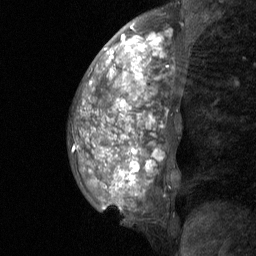
Breast MRI (dynamic contrast-enhanced), one sagittal slice; slice 23 of 64 in the series (ordered by position); dynamic contrast-enhanced study with each time point stored as its own series, time point 2 of 3 at this slice position (early post-contrast, ordered by acquisition time); 1.5 T; TE 4.8 ms, TR 27 ms; 2 mm slice thickness; 256 × 256 image matrix, field of view 180 × 180 mm. Patient: female, 36 years. Case-level facts recorded for this patient, not image findings: setting: breast cancer imaged before/during neoadjuvant chemotherapy; receptor status: HR-positive, HER2-negative.
Structures marked on this image (semi-automatic segmentation, software-assisted and operator-edited):
- analysis volume of interest (the breast-tissue region the enhancement analysis was run in; not a lesion): bounding box (x1, y1, x2, y2) in pixels: (68, 12, 208, 226)
- tumour enhancement mask (voxels above the 90 % enhancement threshold inside the analysis volume of interest): (87, 25, 165, 190)